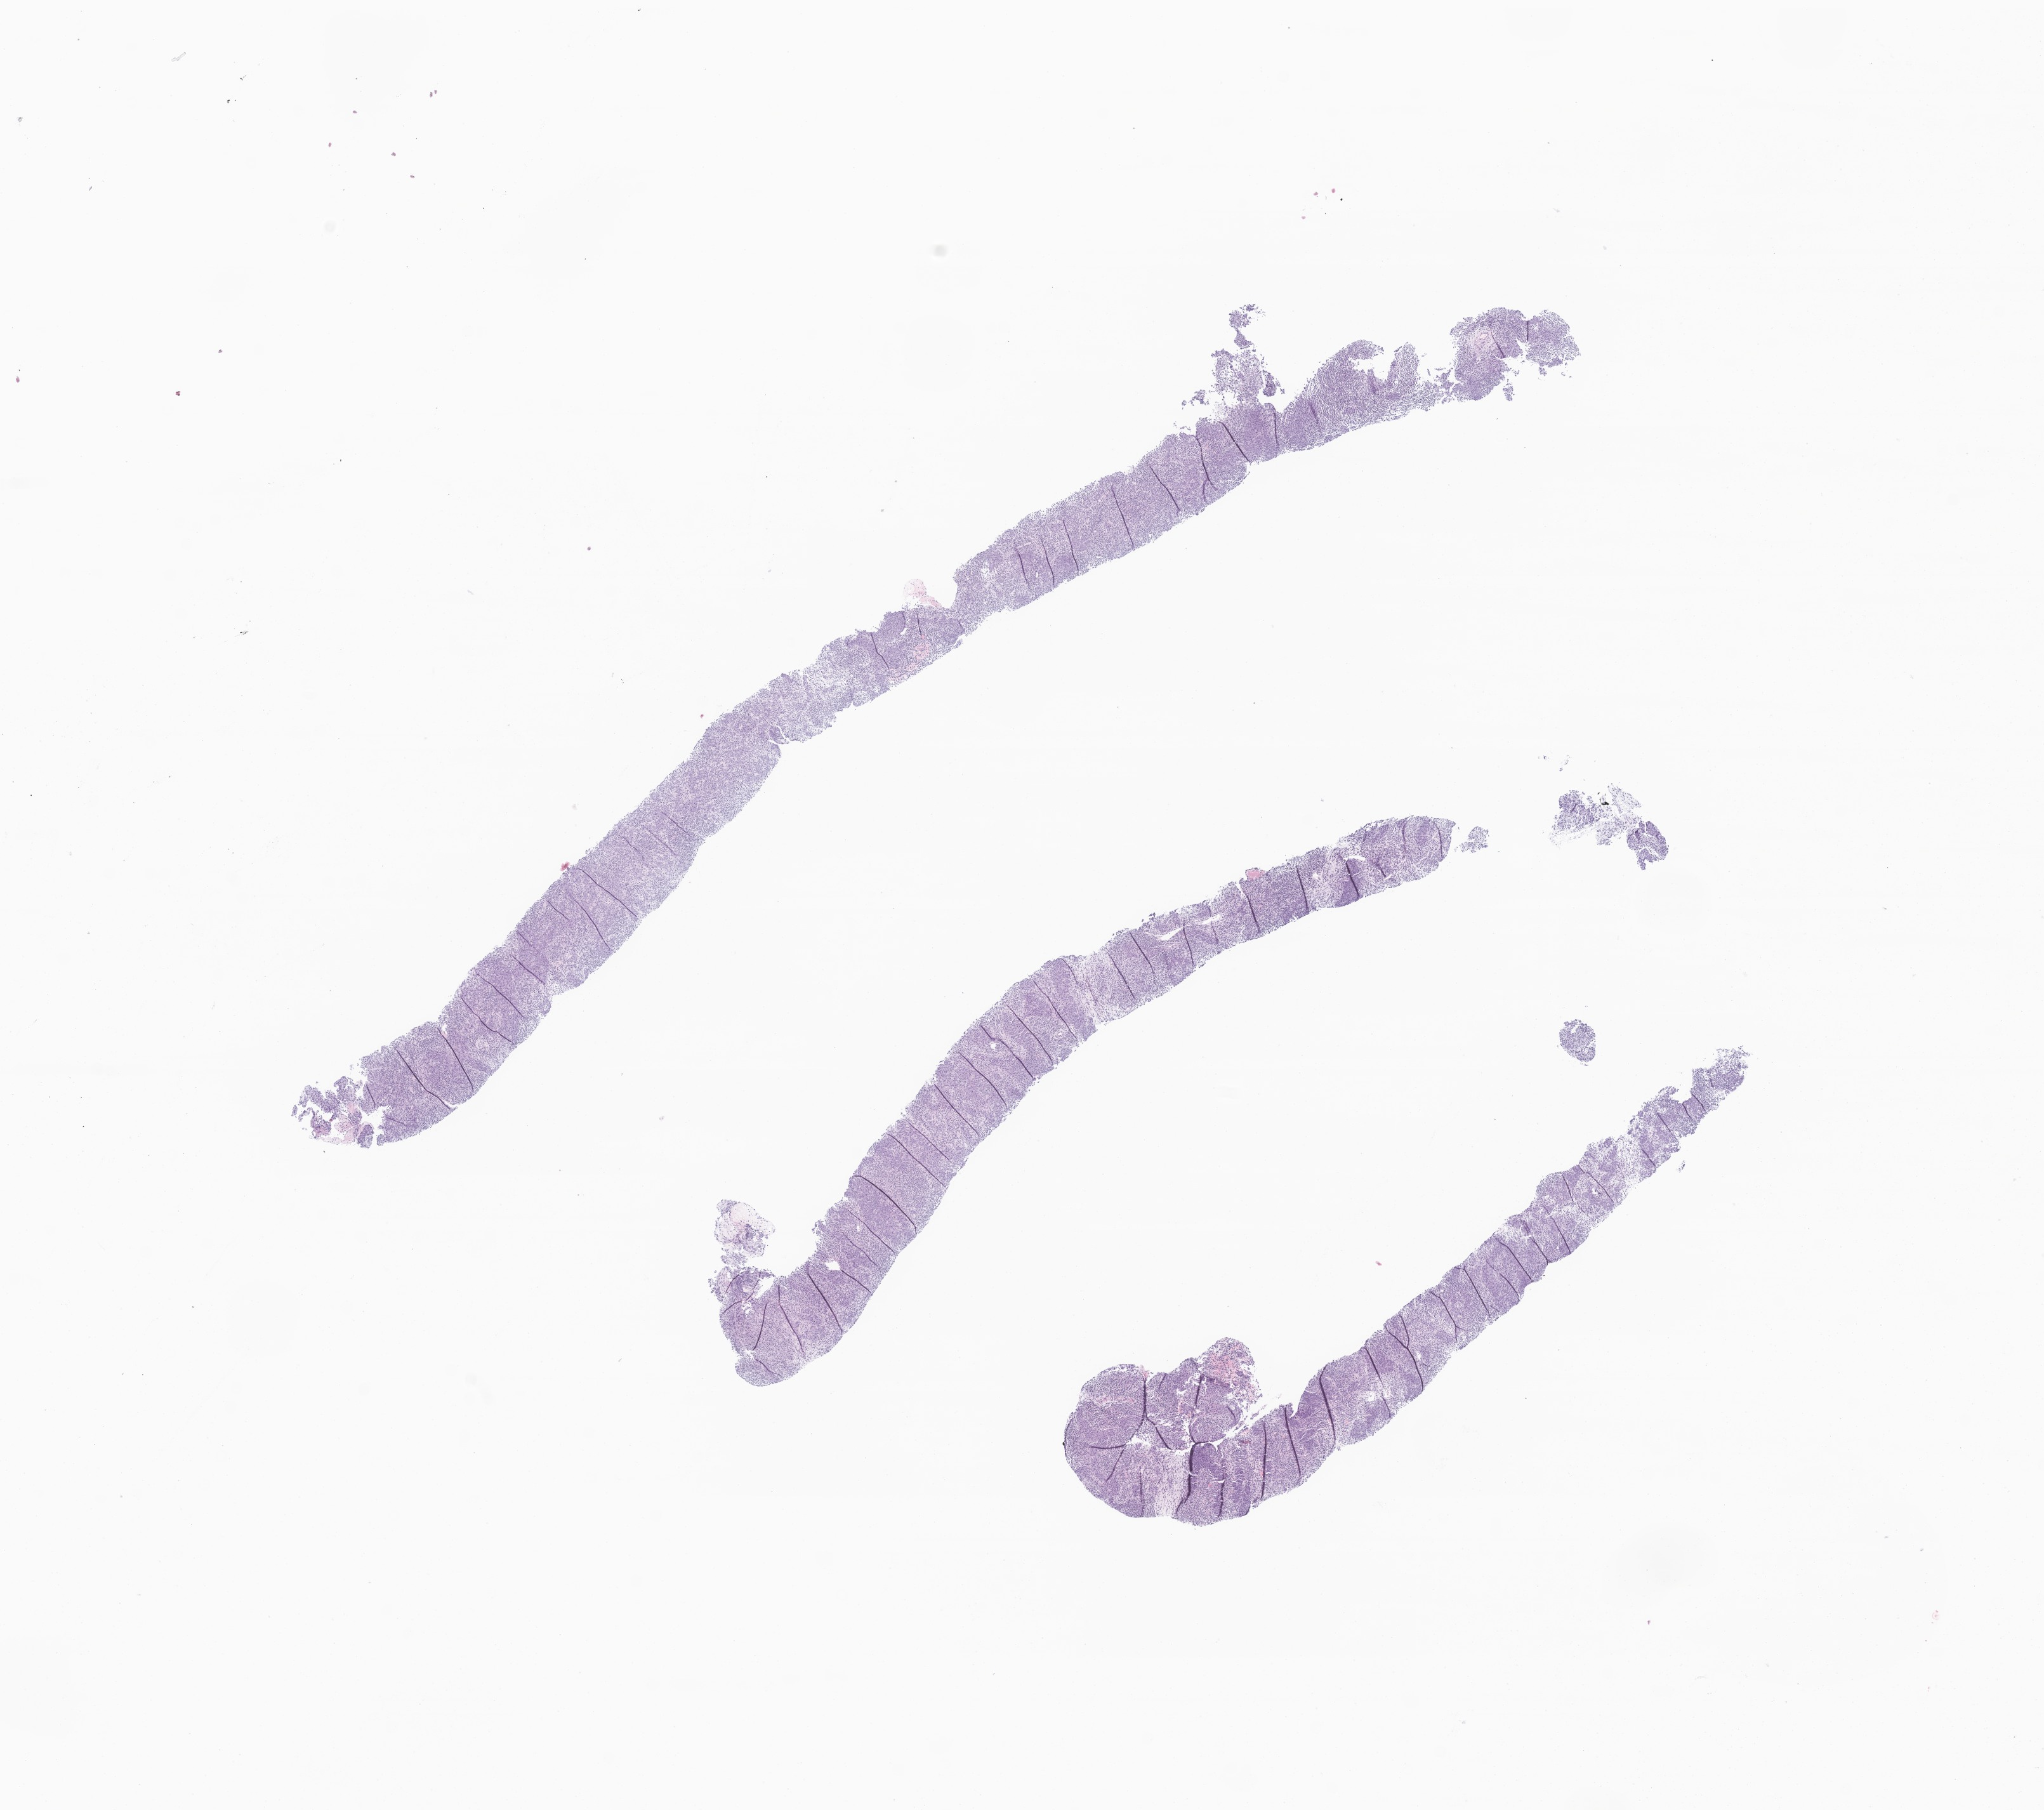
Hematoxylin and eosin (H&E) whole-slide image of tumor tissue from the mediastinum, shown as a low-resolution overview of the whole scanned area (about 13.6 x 12.0 mm). FFPE section. Patient: male, age 139 months (11 years 7 months).
Diagnosis: Carcinoma, NOS.